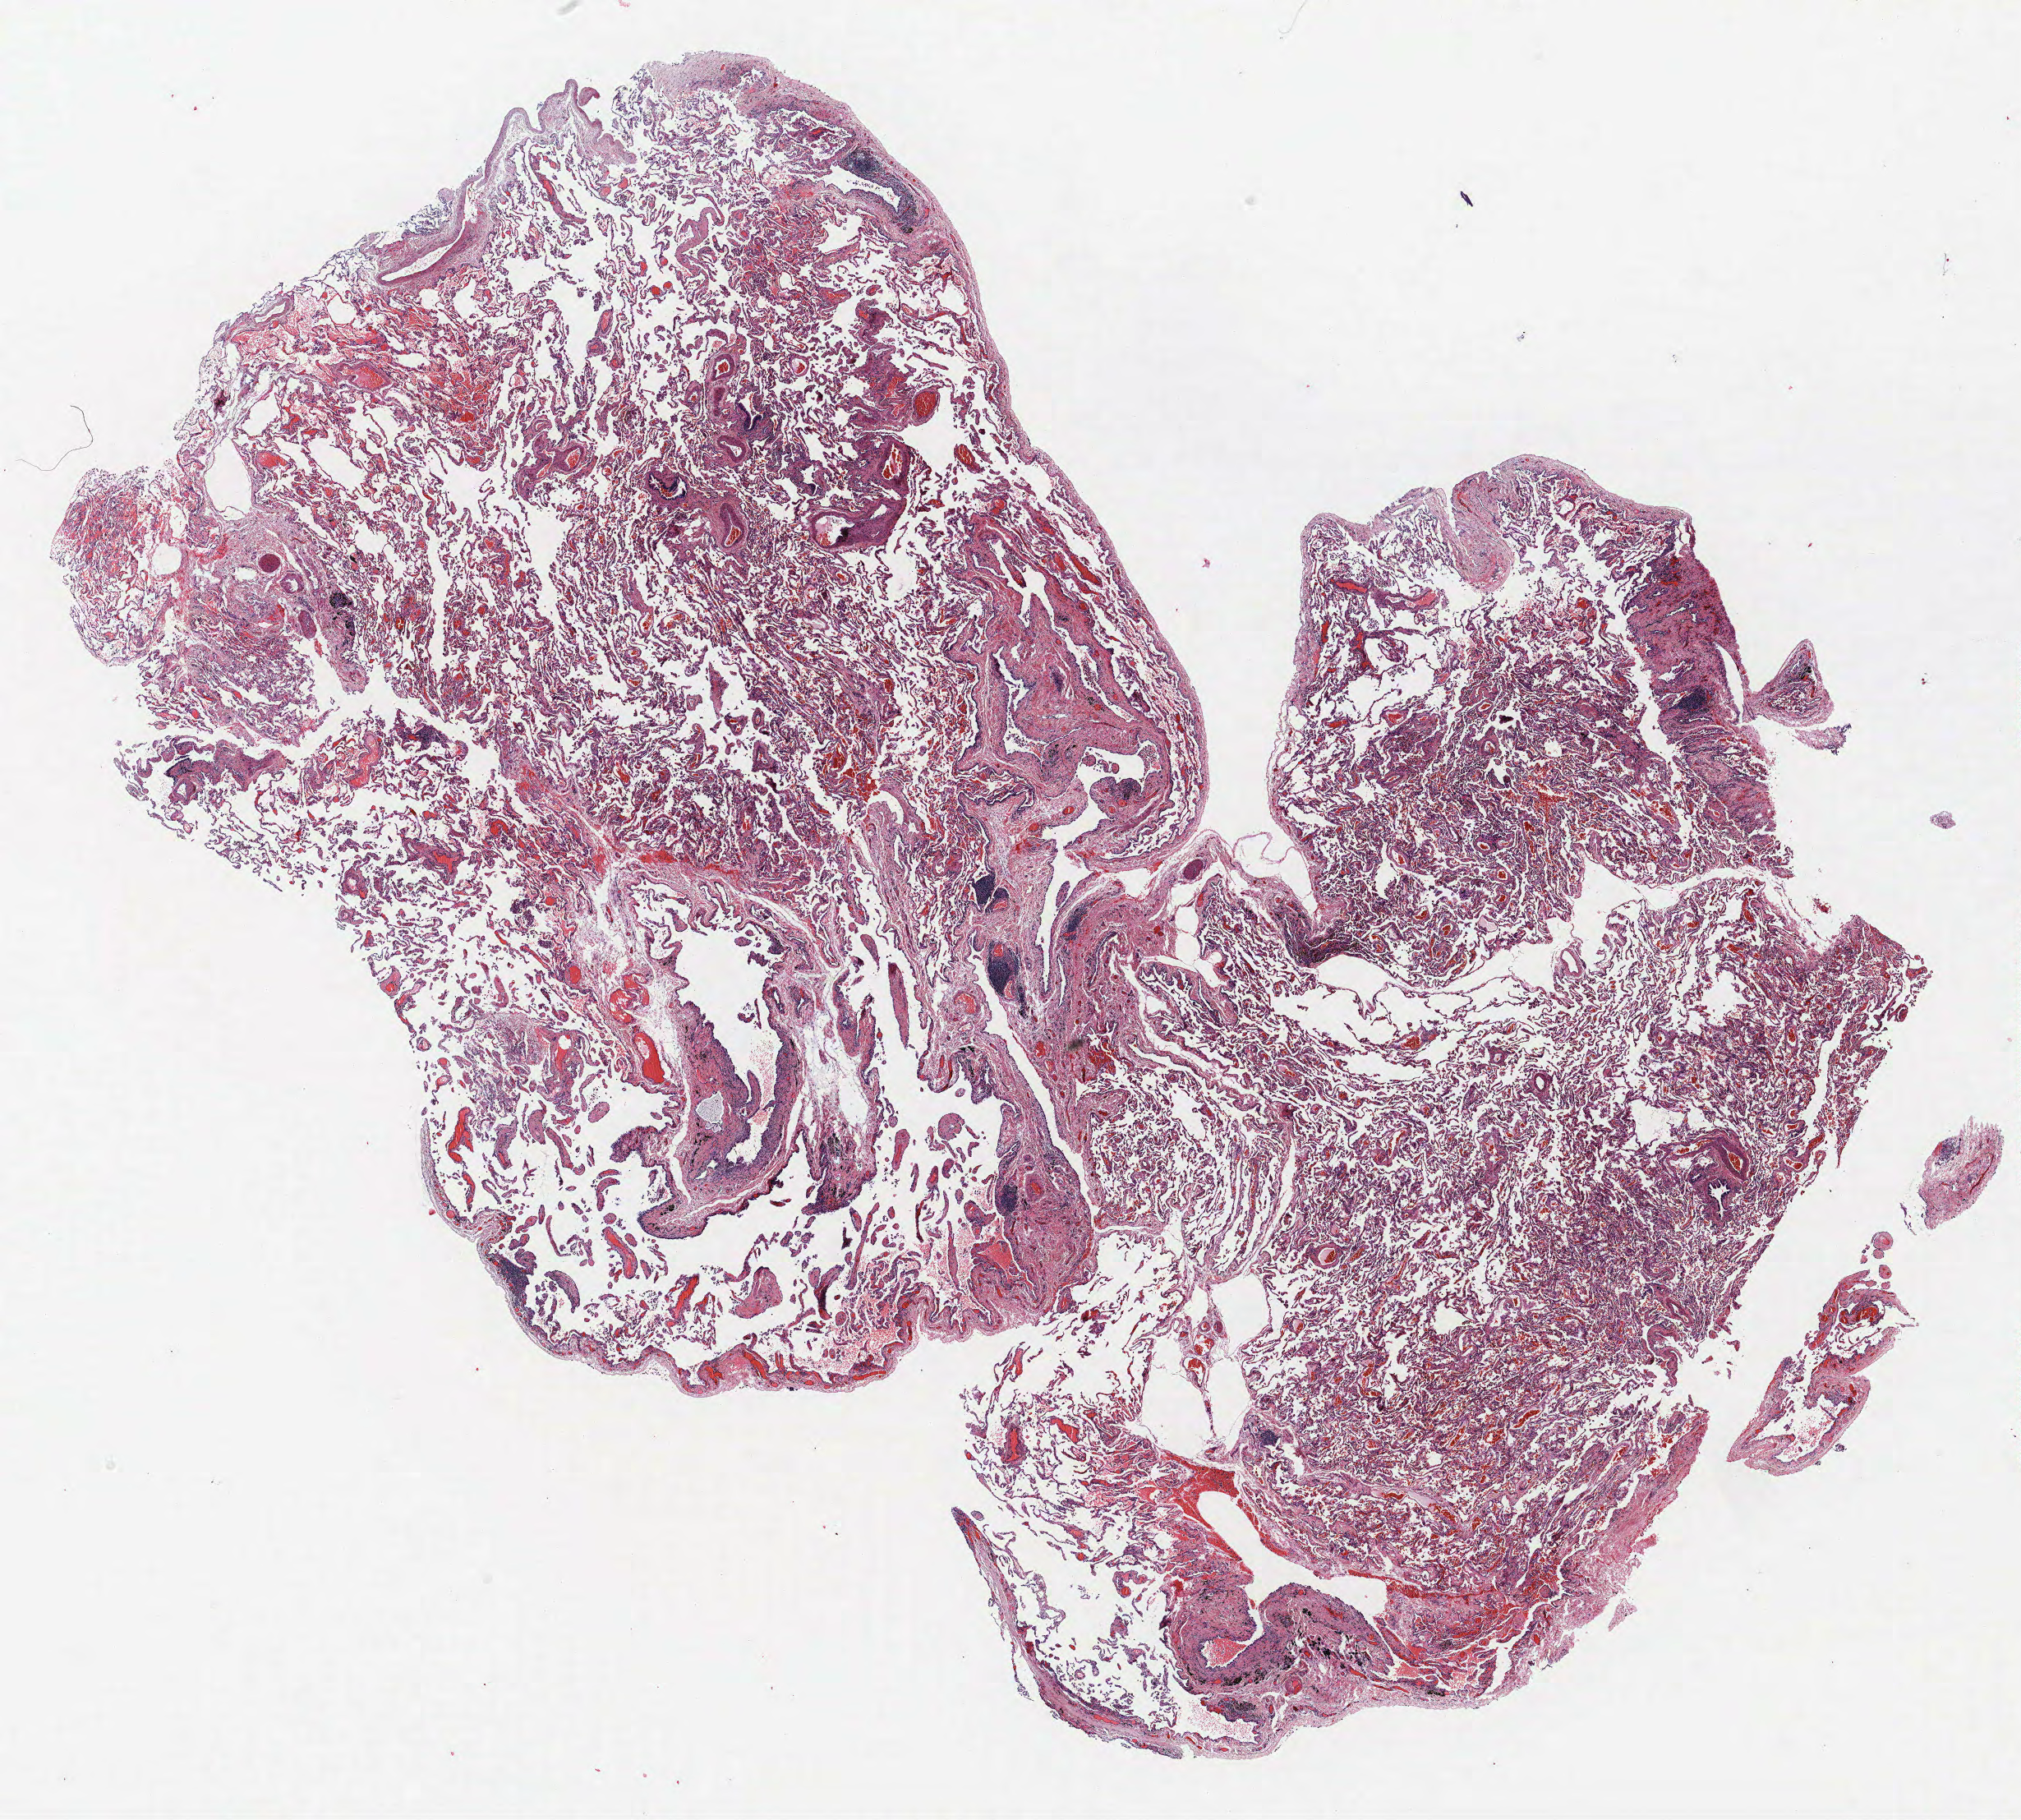
Whole-slide histology image, H&E-stained — whole scanned area (about 19.7 x 17.7 mm) shown as a low-resolution overview. FFPE section. Lung tissue. Female, age 63 at enrolment. Current smoker at enrolment. Grade: moderately differentiated (G2).
ICD-O-3 topography: upper lobe of lung (C34.1). Primary tumour location (clinical record): right upper lobe. Tumour size (pathology): 14 mm. Stage (AJCC 6th edition): IA. Participant's lung-cancer diagnosis: Squamous cell carcinoma, NOS.